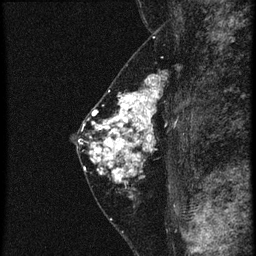
Breast MRI (dynamic contrast-enhanced), one sagittal slice. Position 32 of 60 along the scan axis. 4 images stored at this slice position (order not interpretable as contrast timing). 1.5 T. TE 4.2 ms, TR 20.4 ms. 1.5 mm slice thickness. 256 × 256 image matrix, field of view 180 × 180 mm. Female patient, age 46 years. From the clinical record (not read from this slice): setting: breast cancer imaged before/during neoadjuvant chemotherapy; receptor status: triple-negative.
Annotated regions visible in this slice (semi-automatically segmented with operator editing):
- analysis volume of interest (the breast-tissue region the enhancement analysis was run in; not a lesion): box from (x=88, y=82) to (x=175, y=185) px
- tumour enhancement mask (voxels above the 90 % enhancement threshold inside the analysis volume of interest): (x=90, y=82)–(x=161, y=183)